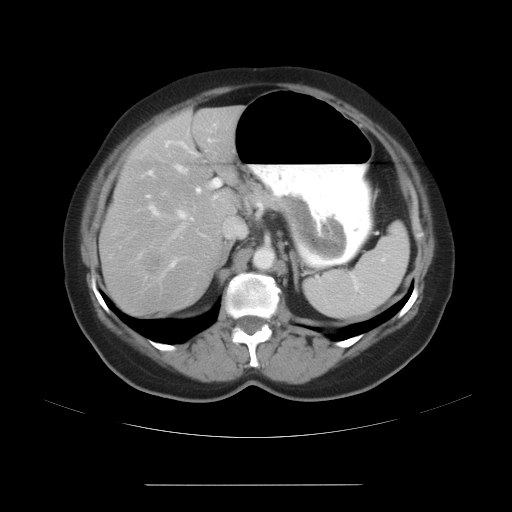
Contrast-enhanced abdominal CT, one axial slice; slice 18 of 27 in the series (ordered by position); intravenous contrast given; soft-tissue window (W 400 / L 40 HU); 512 × 512 image matrix, field of view 440 × 440 mm. Female patient, age 58 years. Case-level facts recorded for this patient, not image findings: diagnosis: colorectal cancer liver metastases, imaged before liver resection; multiple liver metastases: yes; largest metastasis: 1.9 cm; disease in both lobes: yes.
Structures marked on this image (manually delineated by an expert):
- hepatic veins: bounding box (x1, y1, x2, y2) in pixels: (119, 165, 195, 266)
- liver: (102, 110, 238, 313)
- planned liver remnant (the part of the liver to remain after resection): (117, 121, 237, 222)
- portal vein (with intrahepatic branches): (137, 122, 229, 279)
- liver metastasis: (145, 254, 163, 276)